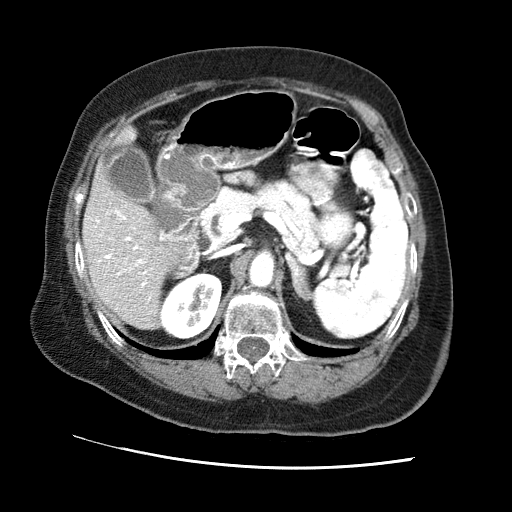
Contrast-enhanced abdominal CT (liver protocol), one axial slice. Slice 30 of 65 in the series (ordered by position). Soft-tissue window (W 400 / L 40 HU). 2.5 mm slice thickness. 512 × 512 image matrix, field of view 340 × 340 mm. Case-level facts recorded for this patient, not image findings: diagnosis: hepatocellular carcinoma (patient treated with transarterial chemoembolisation; whether this scan precedes or follows treatment is not stated here); TNM stage (as recorded): Stage-II; Child-Pugh class: A; tumour differentiation: no biopsy.
Structures marked on this image (semi-automatically segmented with operator editing):
- liver parenchyma outside the tumour (the mass and vessels are separate outlines, so this box may not span the whole liver): bounding box [x1, y1, x2, y2] px = [82, 128, 186, 328]
- liver vessels: [87, 209, 152, 302]